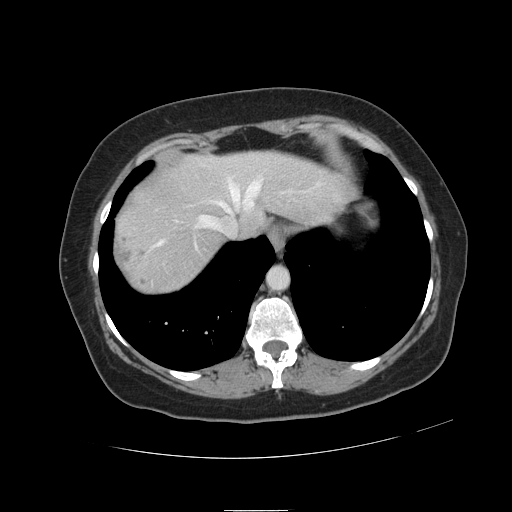
Contrast-enhanced abdominal CT, one axial slice. 120 kVp. Intravenous contrast given. Soft-tissue window (W 400 / L 40 HU). 2.5 mm slice thickness. 512 × 512 image matrix, field of view 400 × 400 mm. Female patient, age 52 years. Case-level facts recorded for this patient, not image findings: diagnosis: colorectal cancer liver metastases, imaged before liver resection; multiple liver metastases: yes.
Annotated regions visible in this slice (expert manual segmentation):
- hepatic veins: bounding box (x1, y1, x2, y2) in pixels: (155, 178, 294, 249)
- liver: (114, 152, 347, 294)
- planned liver remnant (the part of the liver to remain after resection): (177, 152, 345, 233)
- liver metastasis: (117, 250, 130, 268)